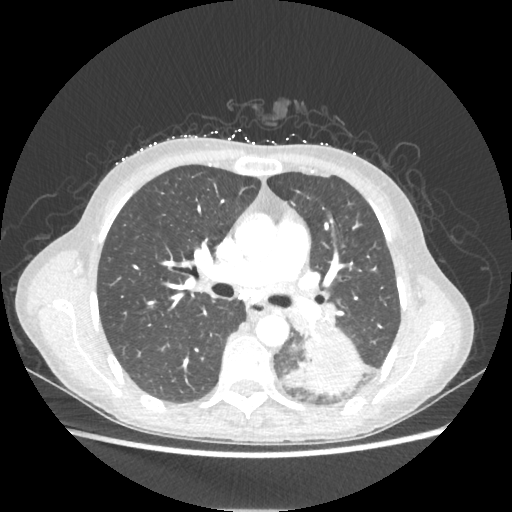
Chest CT, one axial slice; position 131 of 221 along the scan axis; reconstruction kernel STANDARD; lung window (W 1500 / L -600 HU); 512 × 512 image matrix, field of view 360 × 360 mm. Patient: female, 53 years. Case-level facts recorded for this patient, not image findings: clinical TNM (as recorded): T3 N0 M0.
Annotated regions visible in this slice (bounding box drawn by a radiologist):
- lung tumour (recorded histology: adenocarcinoma): bounding box <287,333,368,396> (left, top, right, bottom; pixels)